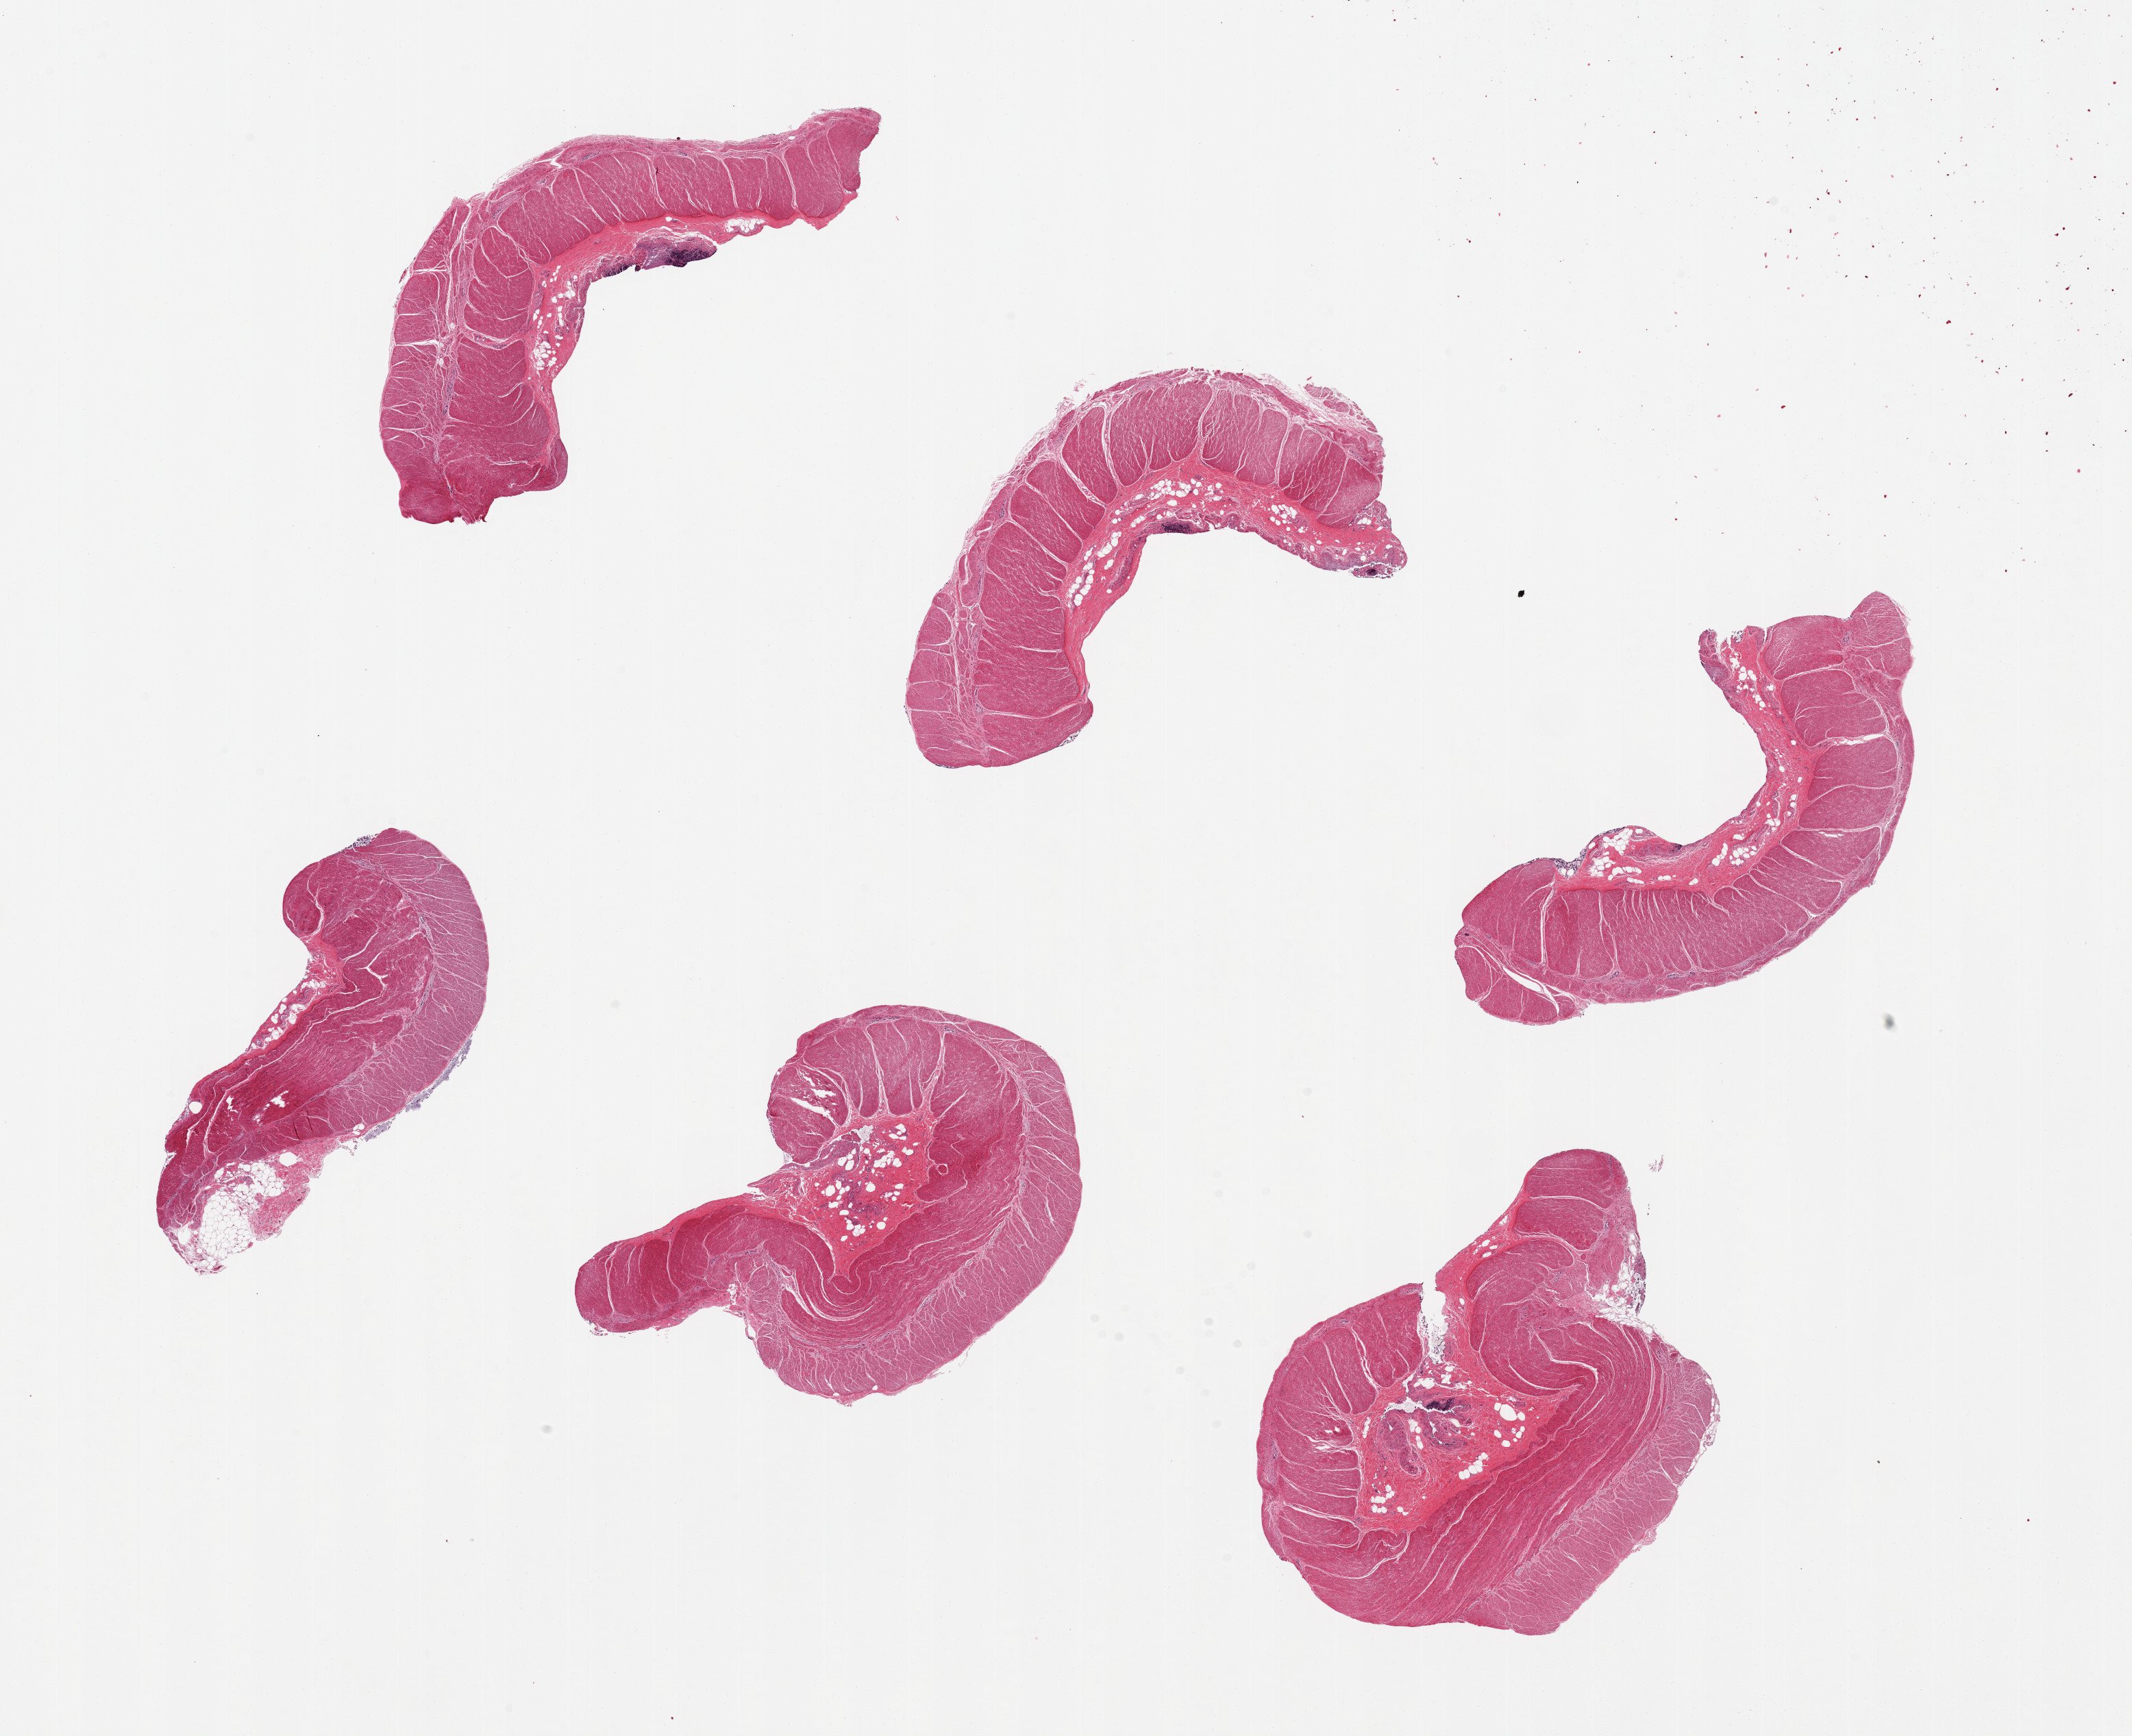
Digitized hematoxylin and eosin (H&E)-stained section — whole scanned area (about 24.6 x 20.0 mm, slide scanned at 20x) shown as a low-resolution overview, PAXgene-fixed paraffin-embedded (PFPE) section, section of sigmoid colon (target tissue), donor tissue sample. Female donor.
Review note (as recorded): 6 pieces, all muscularis propria, excellent specimens.